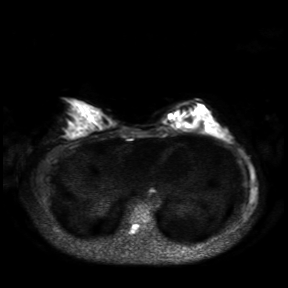
Breast MRI, one axial slice; position 12 of 30 along the scan axis; diffusion-weighted series; image 2 of 4 stored at this slice position (different b-values; order by instance number); 3 T; 4 mm slice thickness; 288 × 288 image matrix, field of view 360 × 360 mm. Female patient.
Annotated regions visible in this slice (expert manual segmentation):
- tumour on diffusion-weighted imaging: bounding box [x1, y1, x2, y2] px = [168, 112, 178, 121]